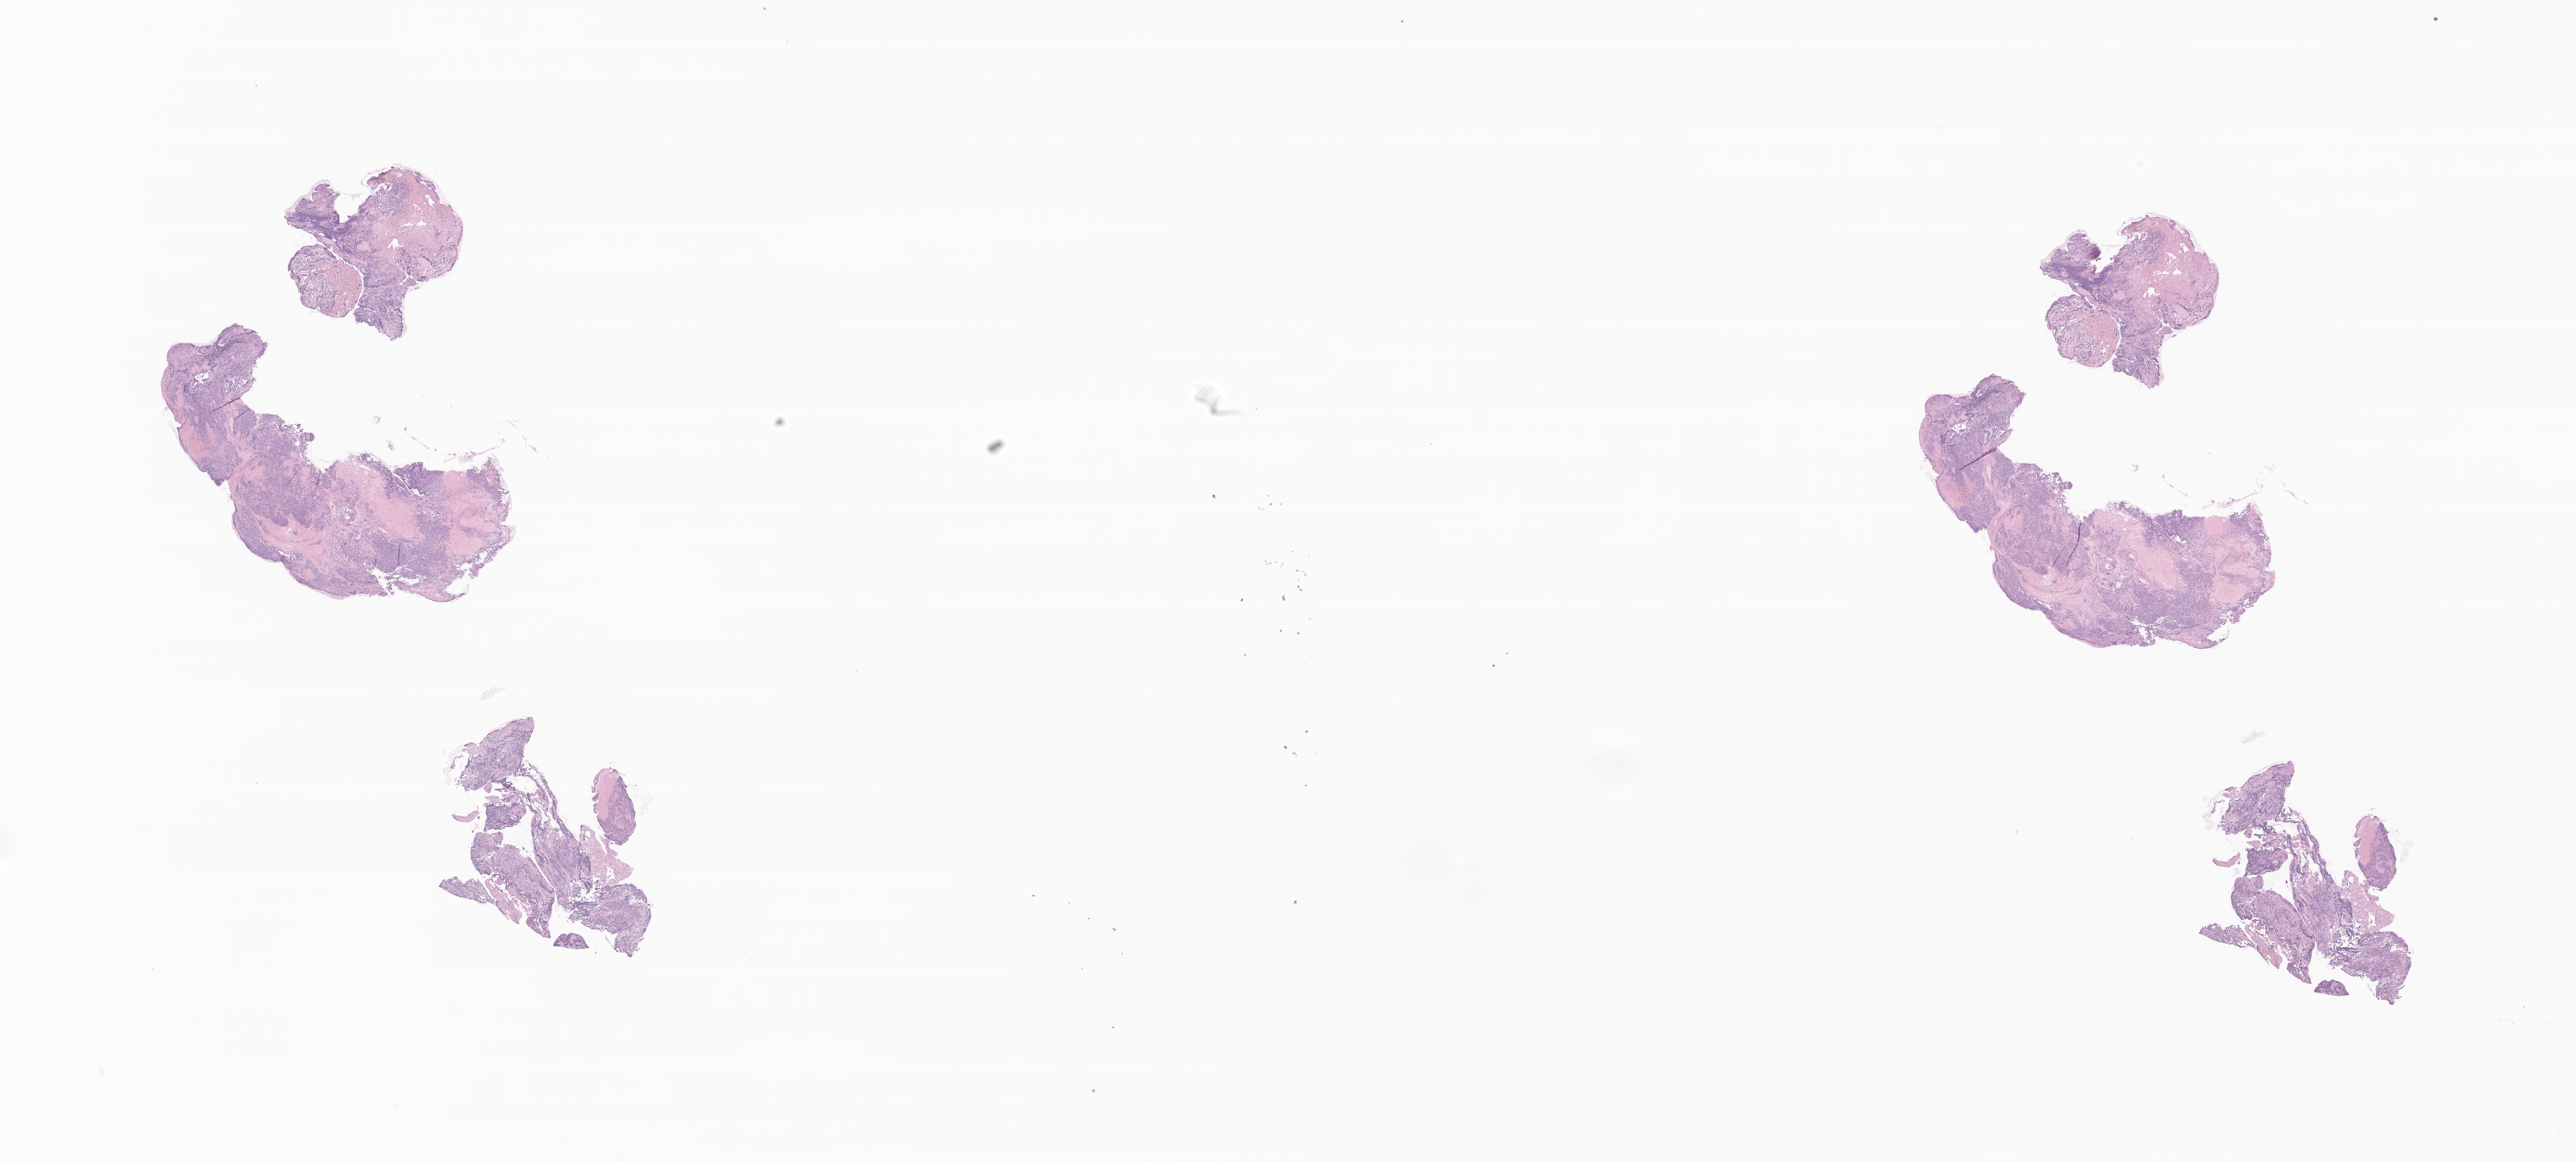
Digitized hematoxylin and eosin (H&E)-stained section of tumor tissue from the brain, low-resolution overview of the scanned area, about 29.6 x 13.4 mm; formalin-fixed, paraffin-embedded (FFPE) tissue. Patient: male, age 97 months (8 years 1 month).
Diagnosis (ICD-O-3 morphology term): Medulloblastoma, NOS.